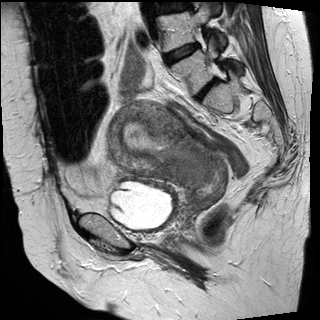
Pelvic MRI for cervical cancer, one sagittal slice. Slice 18 of 30 in the series (ordered by position). T2-weighted. 1.5 T. TE 89 ms, TR 3810 ms. 4 mm slice thickness. 320 × 320 image matrix. Female patient, age 62 years.
Annotated regions visible in this slice (manually delineated by an expert):
- uterus and cervix: bounding box (x1, y1, x2, y2) in pixels: (108, 99, 229, 208)